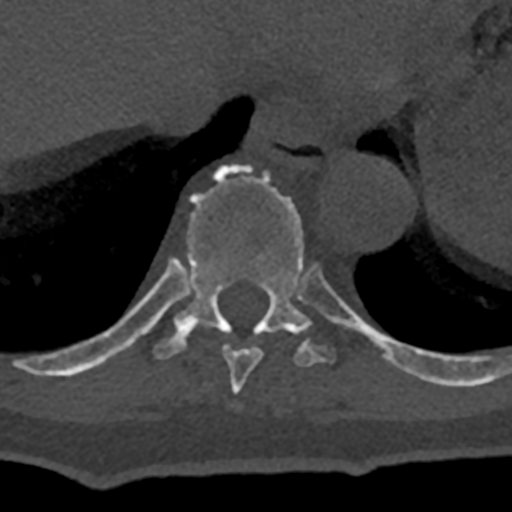
CT including the spine, one axial slice; position 621 of 797 along the scan axis; reconstruction kernel Br40s/3; 120 kVp; bone window (W 1800 / L 400 HU); 0.5 mm slice thickness; 512 × 512 image matrix, field of view 160 × 160 mm. Male patient, age 74 years. From the clinical record (not read from this slice): primary cancer: renal; vertebrae with lytic lesions (as recorded): T10, L1, L2, L3, L4, L5.
Annotated regions visible in this slice (semi-automatically segmented with operator editing):
- T10 vertebra: bounding box [x1, y1, x2, y2] px = [70, 164, 432, 382]
- T9 vertebra: [185, 327, 263, 394]